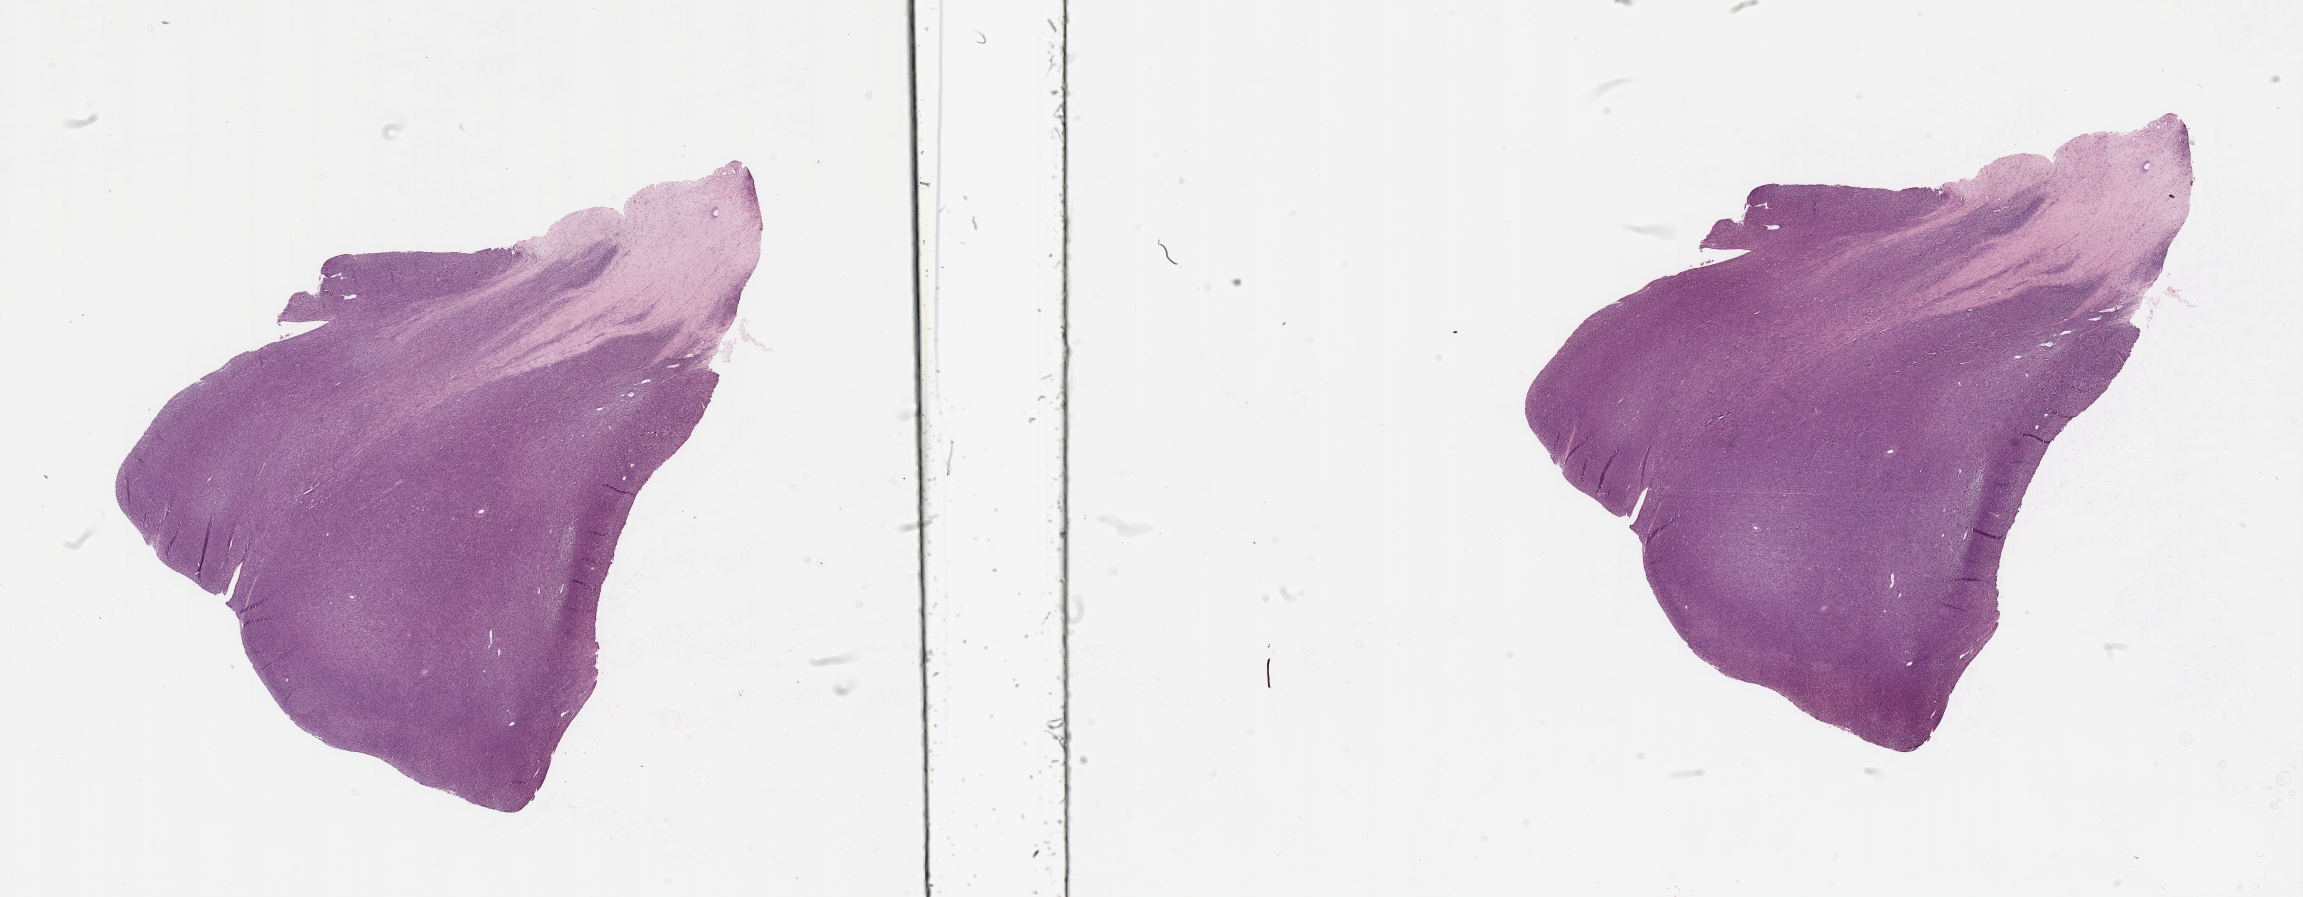
Hematoxylin and eosin (H&E) stained whole-slide image, low-resolution overview of the scanned area, about 36.4 x 14.2 mm (slide scanned at 20x). Tumour tissue sample. Patient: female, age 52 years.
Patient diagnosis (cohort enrolment): sarcoma (site not recorded at cohort level).